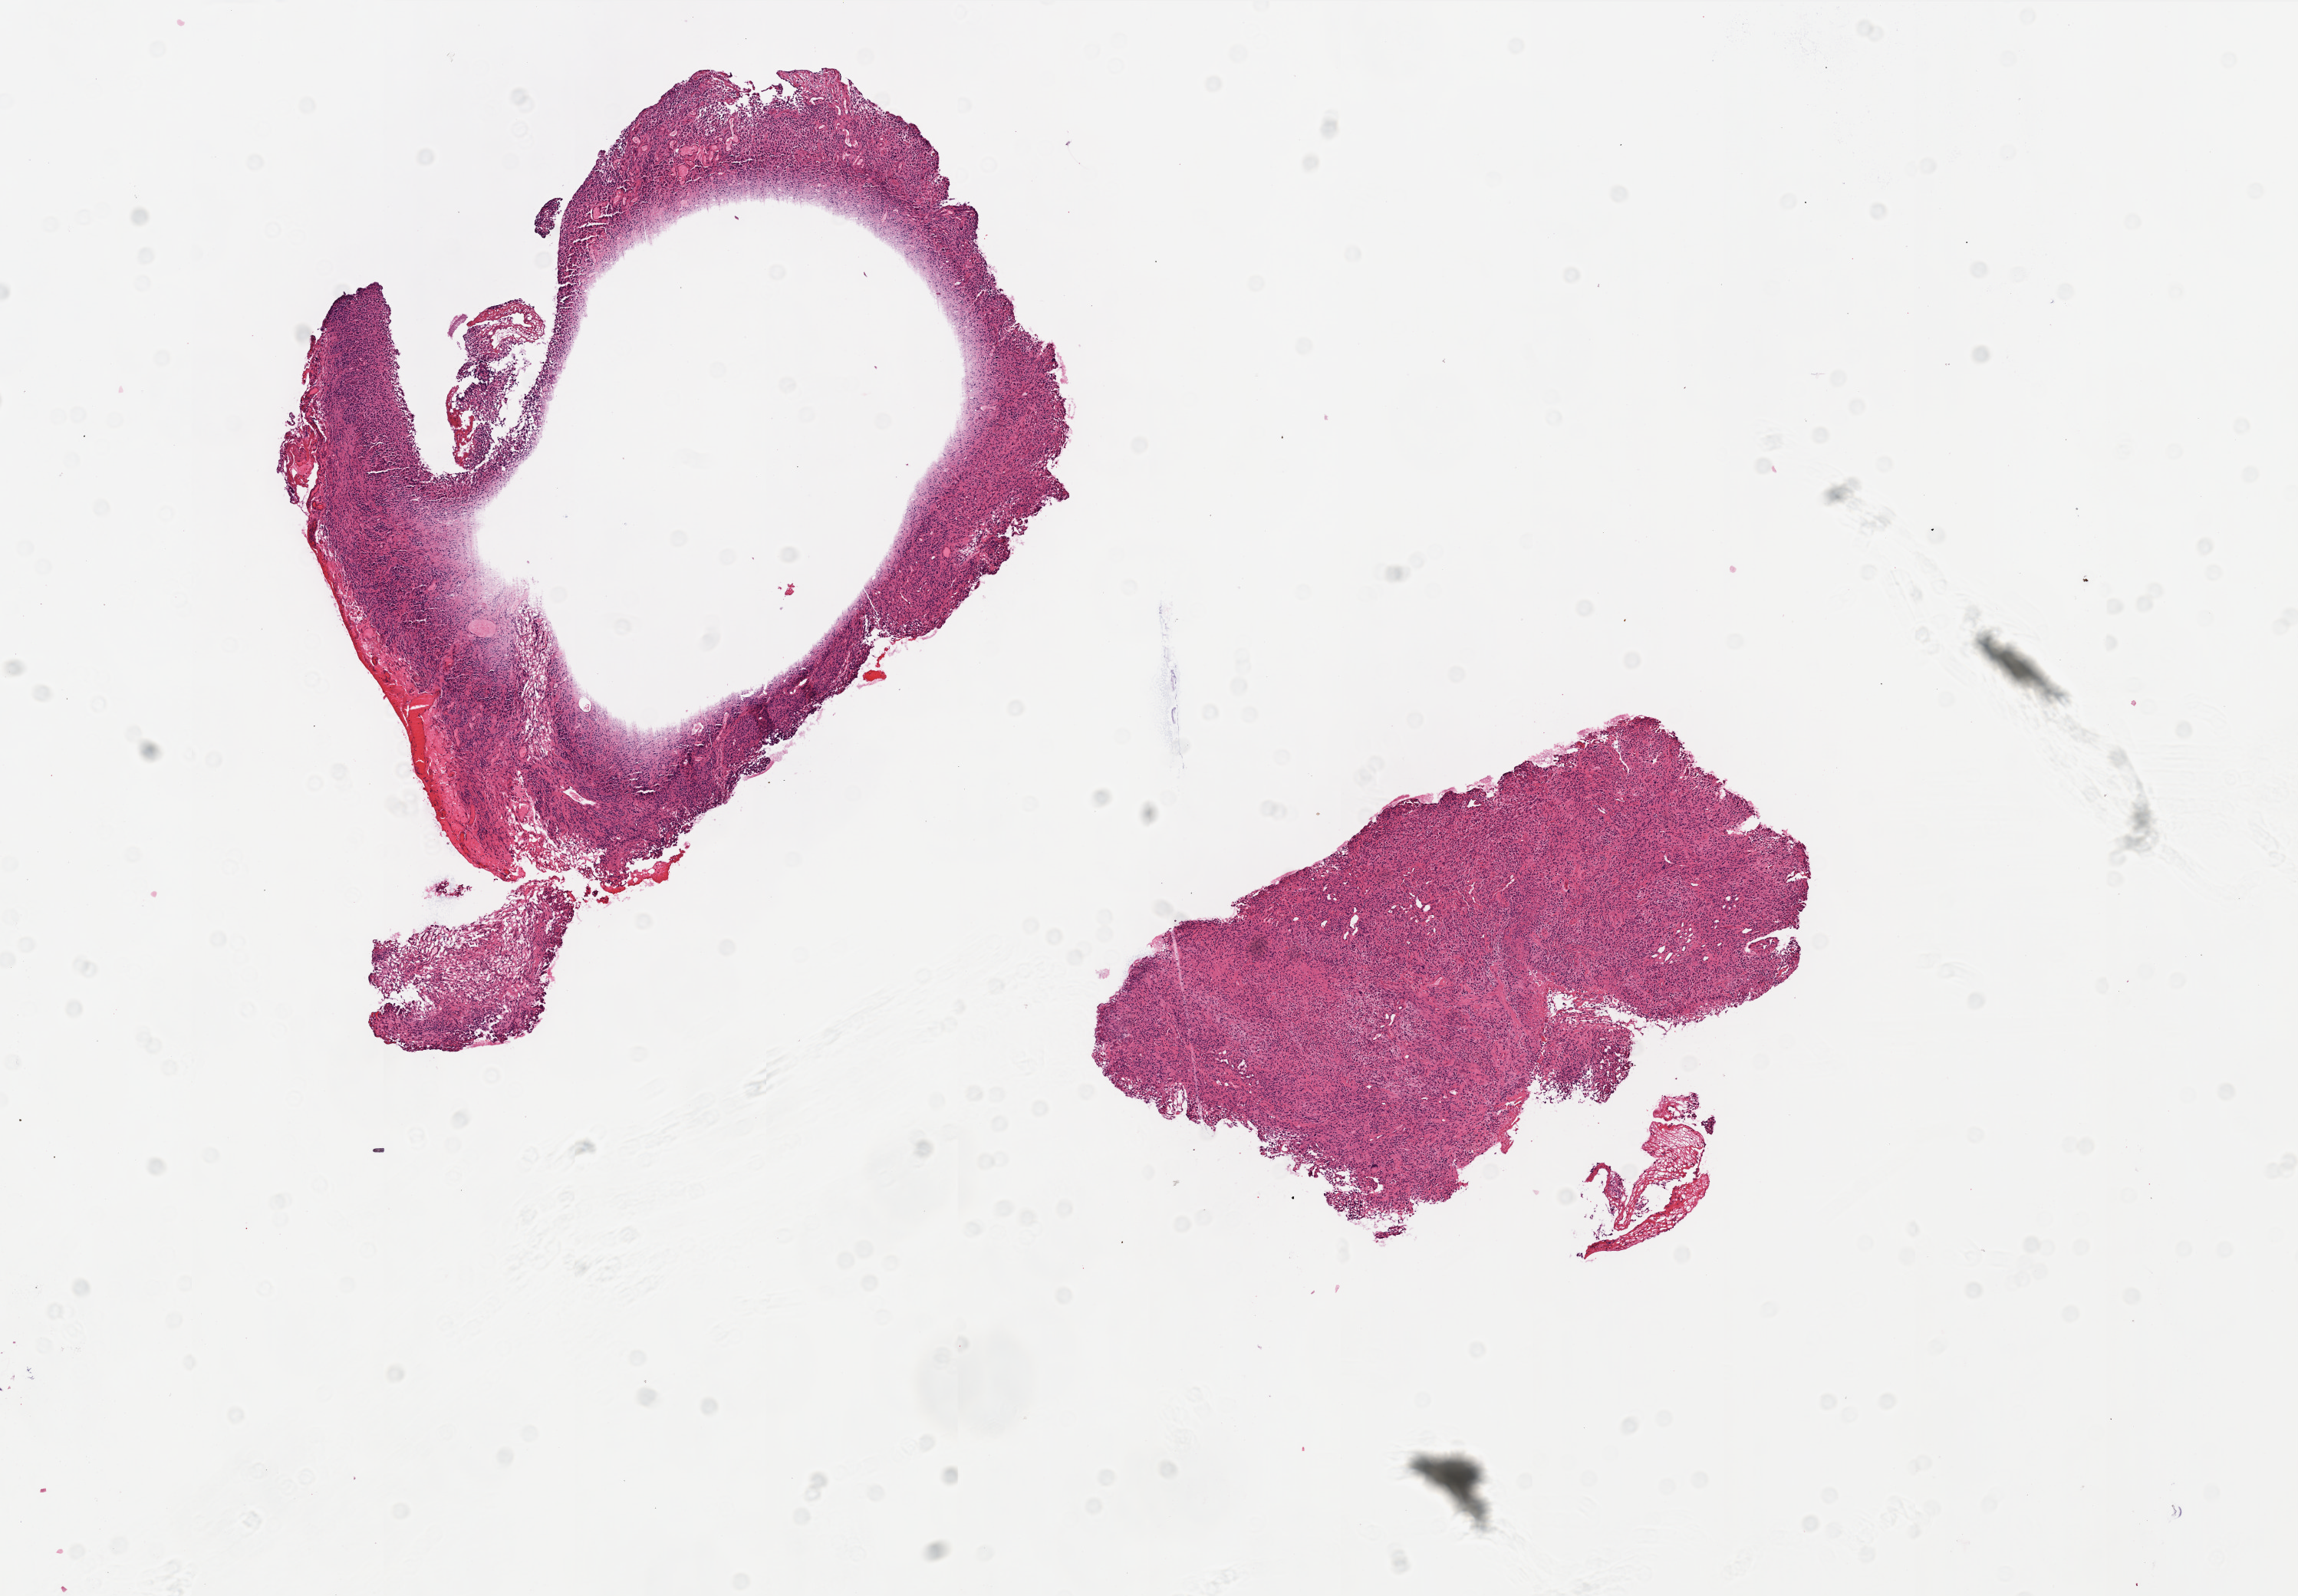
H&E-stained whole-slide image — low-resolution overview of the scanned area, about 12.0 x 8.3 mm; formalin-fixed paraffin-embedded (FFPE) diagnostic section; primary tumour sample from the brain. Female patient; age at initial diagnosis 52 years.
Diagnosis: Glioblastoma.